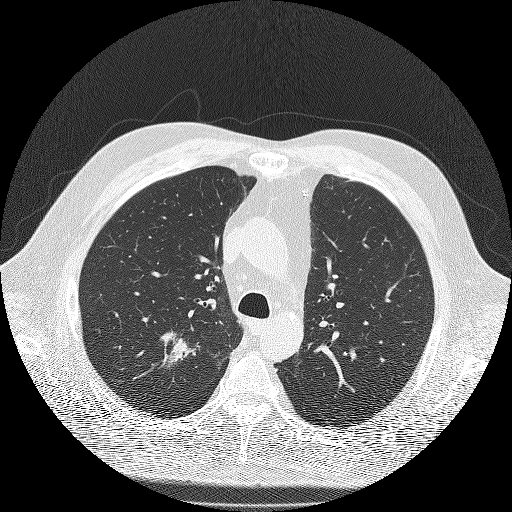
Chest CT (low-dose screening protocol), one axial image. Second annual screen. Lung window (W 1500 / L -600 HU). 2 mm slice thickness. 120 kVp. Slice 41 of 180 in the series. 512 × 512 image matrix, field of view 385 × 385 mm. Male participant, aged 71 years at enrolment. Former smoker at enrolment.
Expert reader's lesion annotation, bounding box [x1, y1, x2, y2] px = [135, 324, 209, 389]. The screening reader recorded 3 non-calcified nodules or masses ≥4 mm on this exam (right upper lobe, right upper lobe, right lower lobe); which of them this box marks is not recorded. Official screen result: positive, other. Later outcome: lung cancer diagnosed 59 days after this screen — bronchiolo-alveolar adenocarcinoma, NOS, right upper lobe, moderately differentiated (G2), stage IIIA (AJCC 6th edition), 25 mm at pathology.